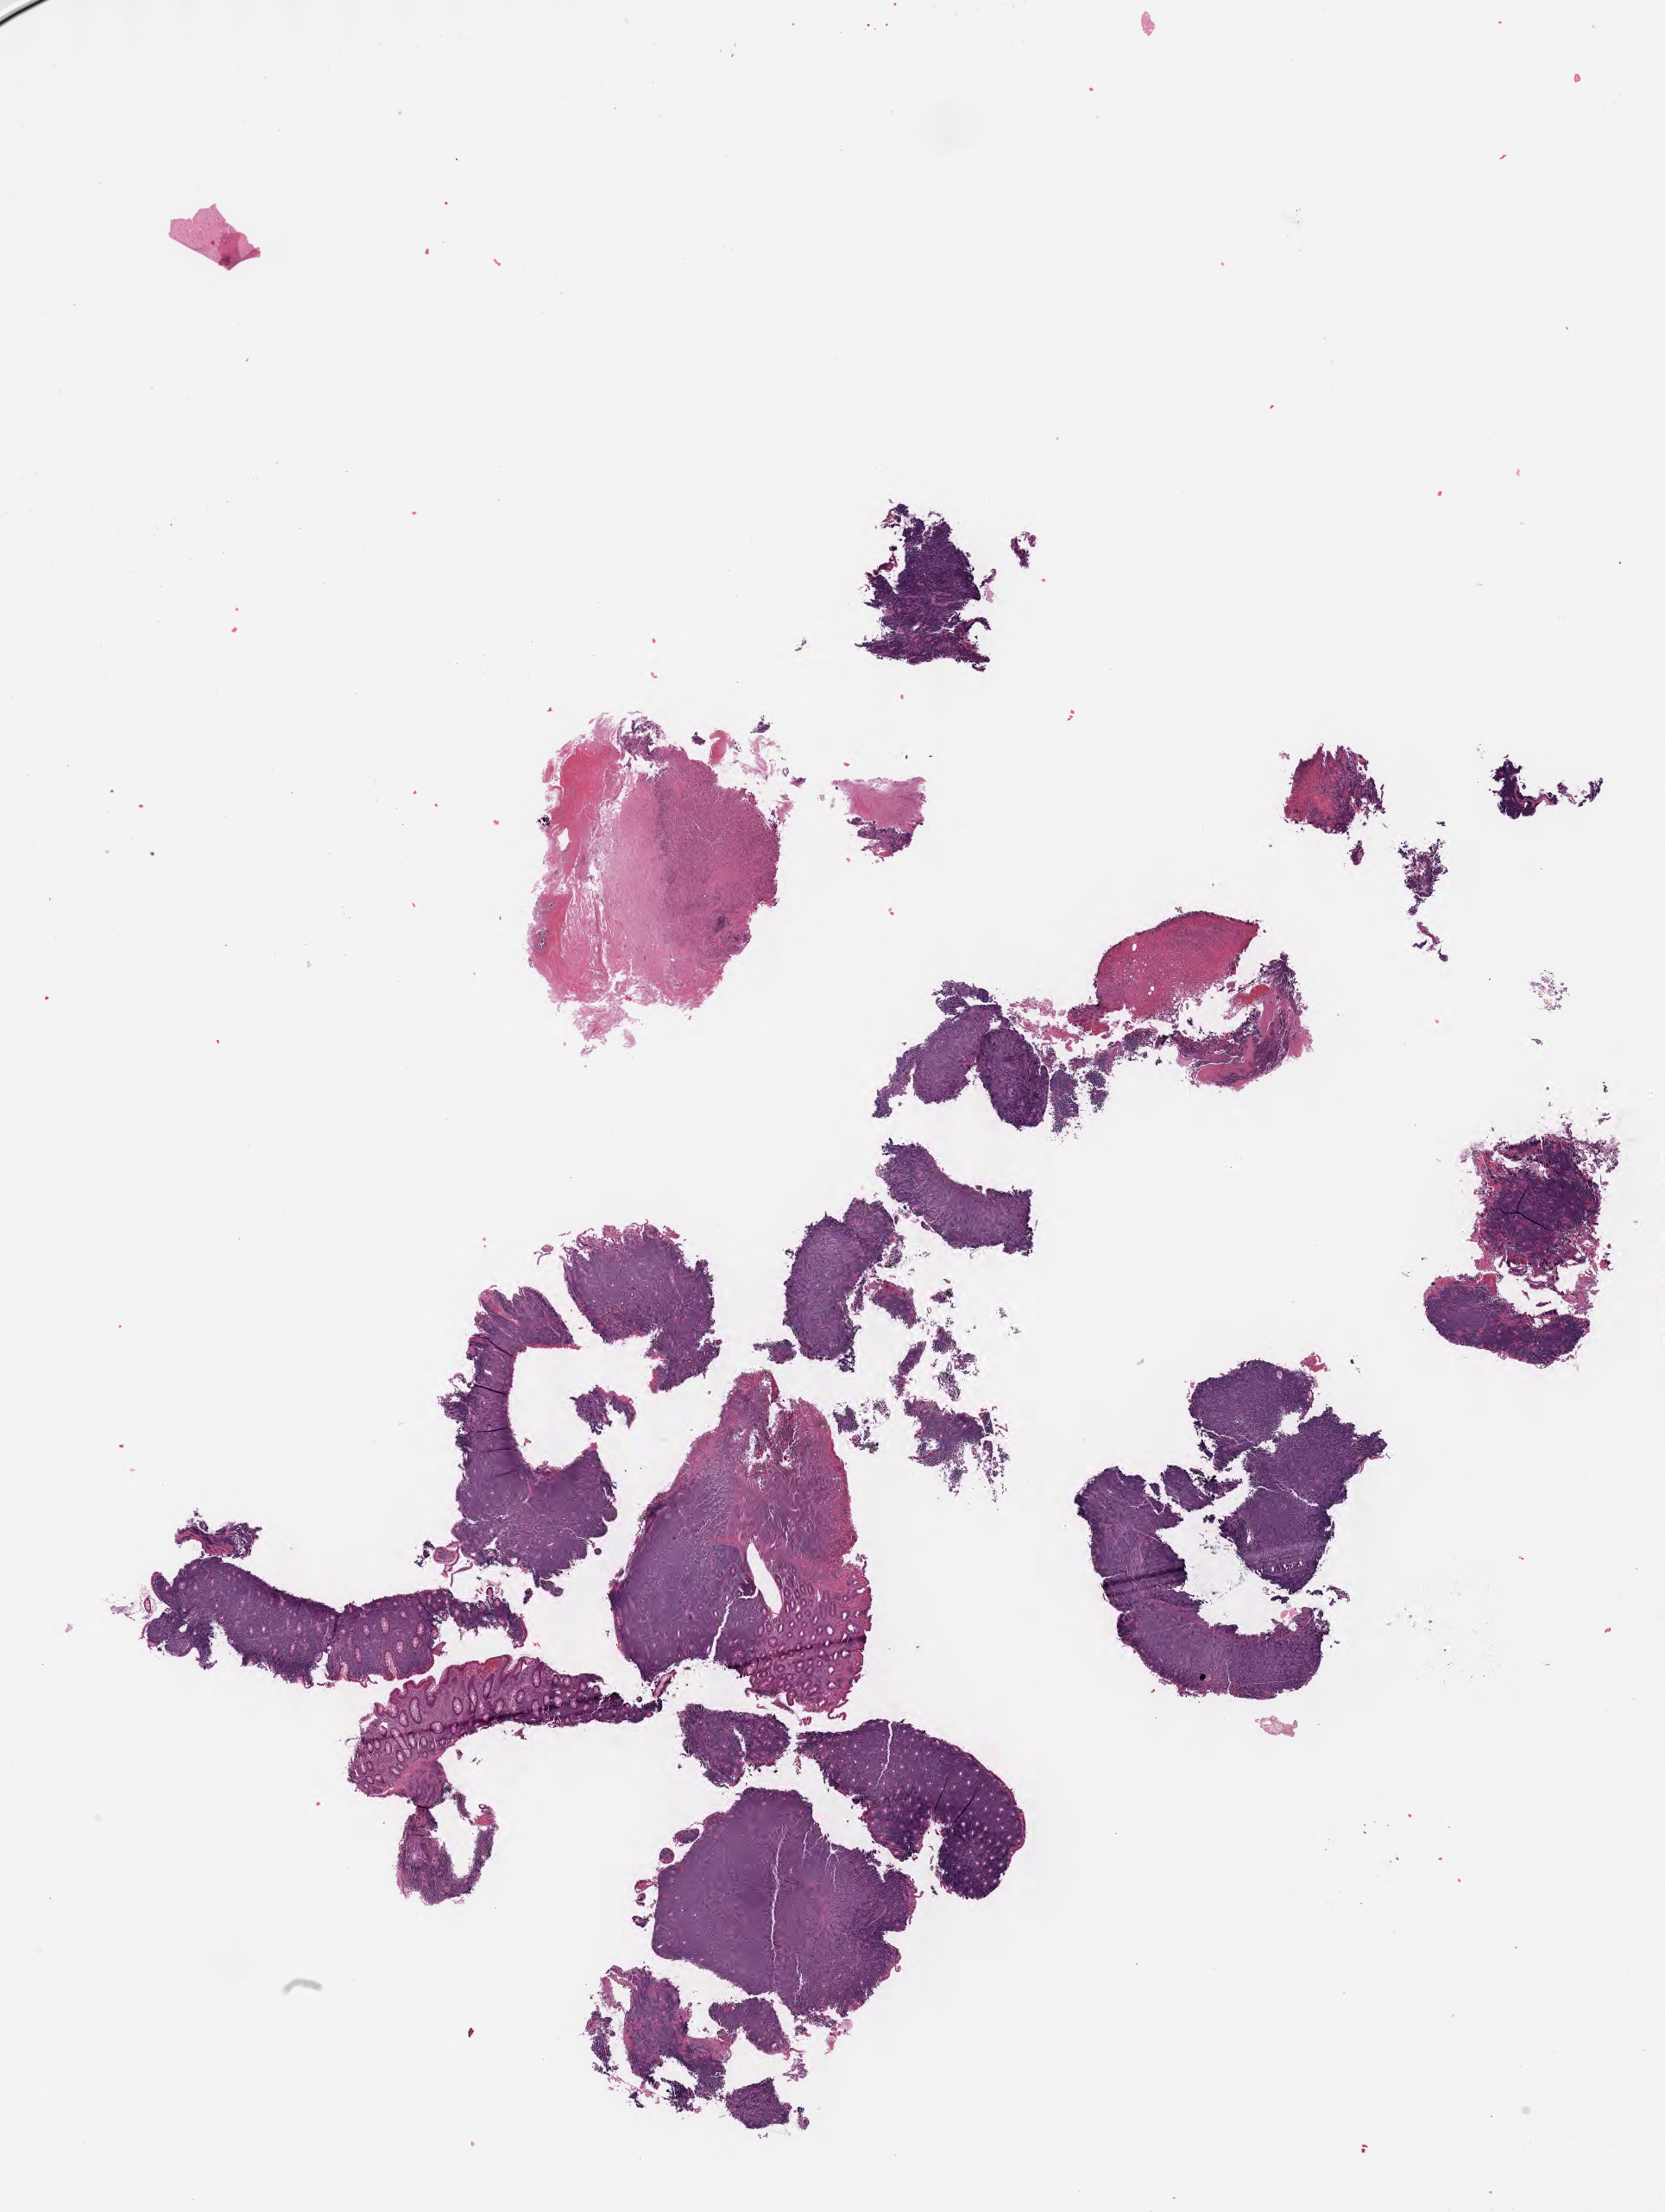
Haematoxylin and eosin whole-slide image — a low-resolution overview of the entire scanned area, about 15.6 x 20.7 mm. Tumor tissue. Patient: male, 56 years old.
Diagnosis: Burkitt lymphoma, NOS.